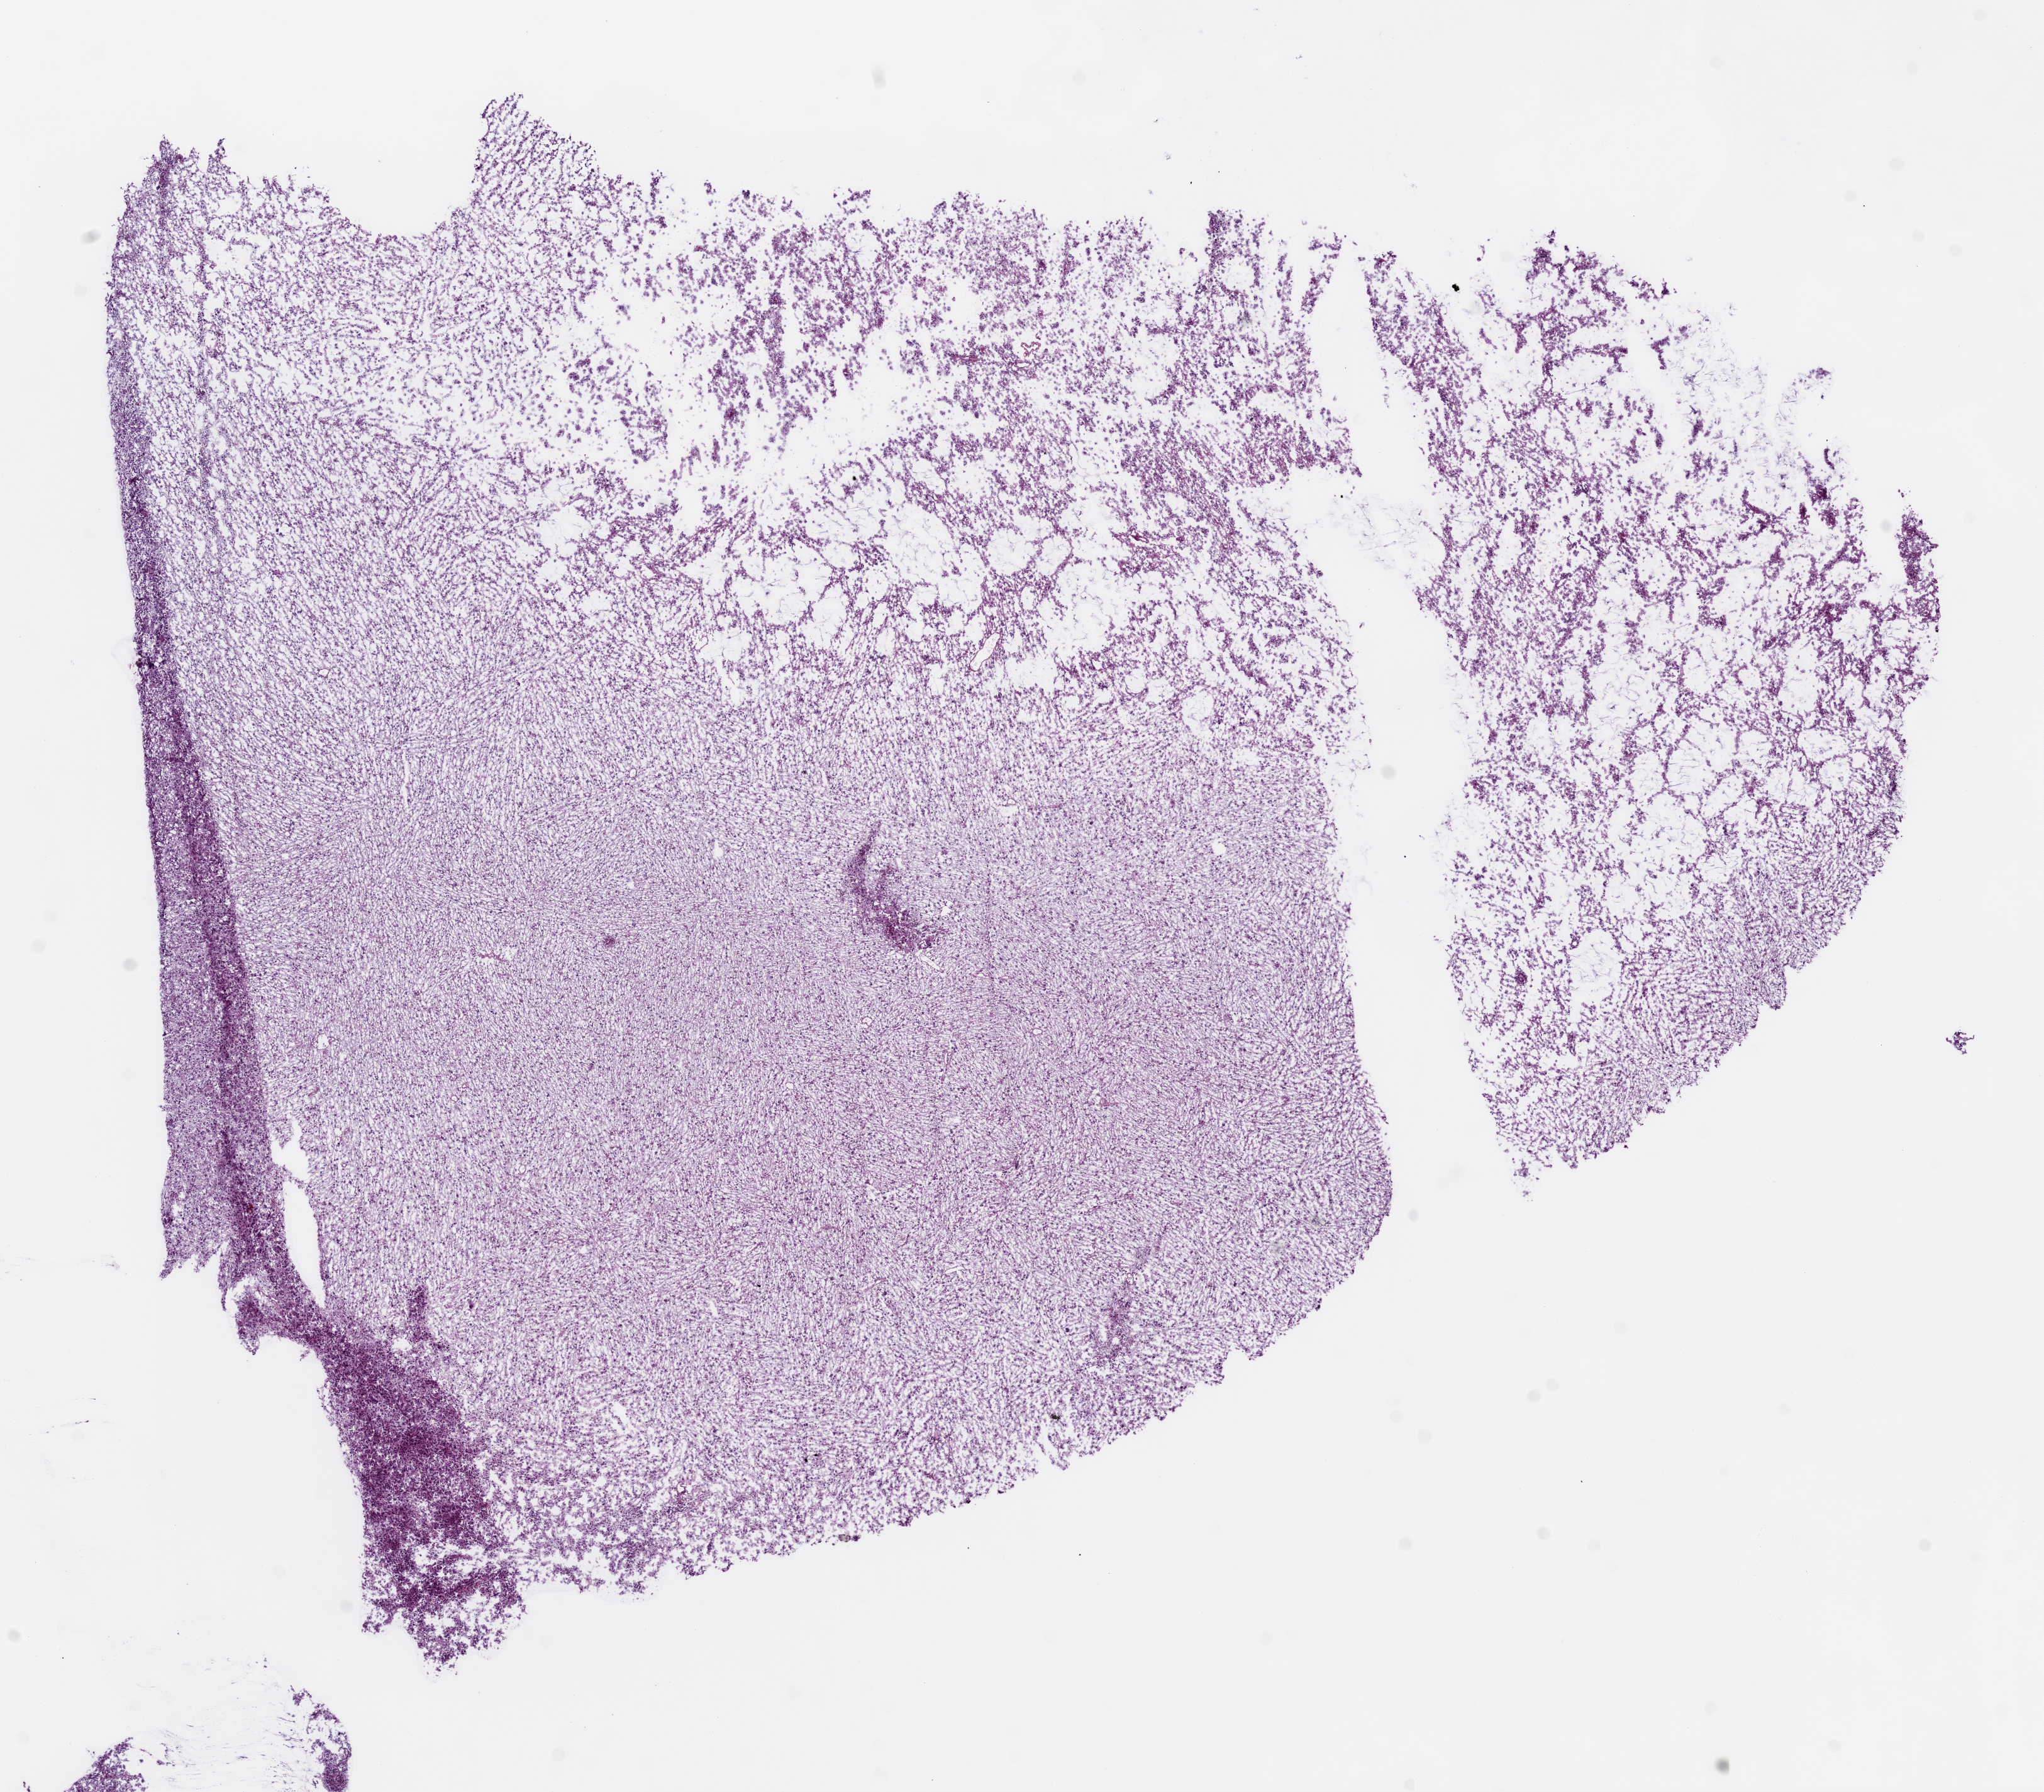
Hematoxylin and eosin (H&E) stained whole-slide image, whole scanned area (about 13.0 x 11.4 mm, slide scanned at 20x) shown as a low-resolution overview, frozen section from the top of the tissue portion, sample: primary tumour, brain. Male patient; age at initial diagnosis 34 years.
Diagnosis: Astrocytoma, anaplastic (cerebrum).